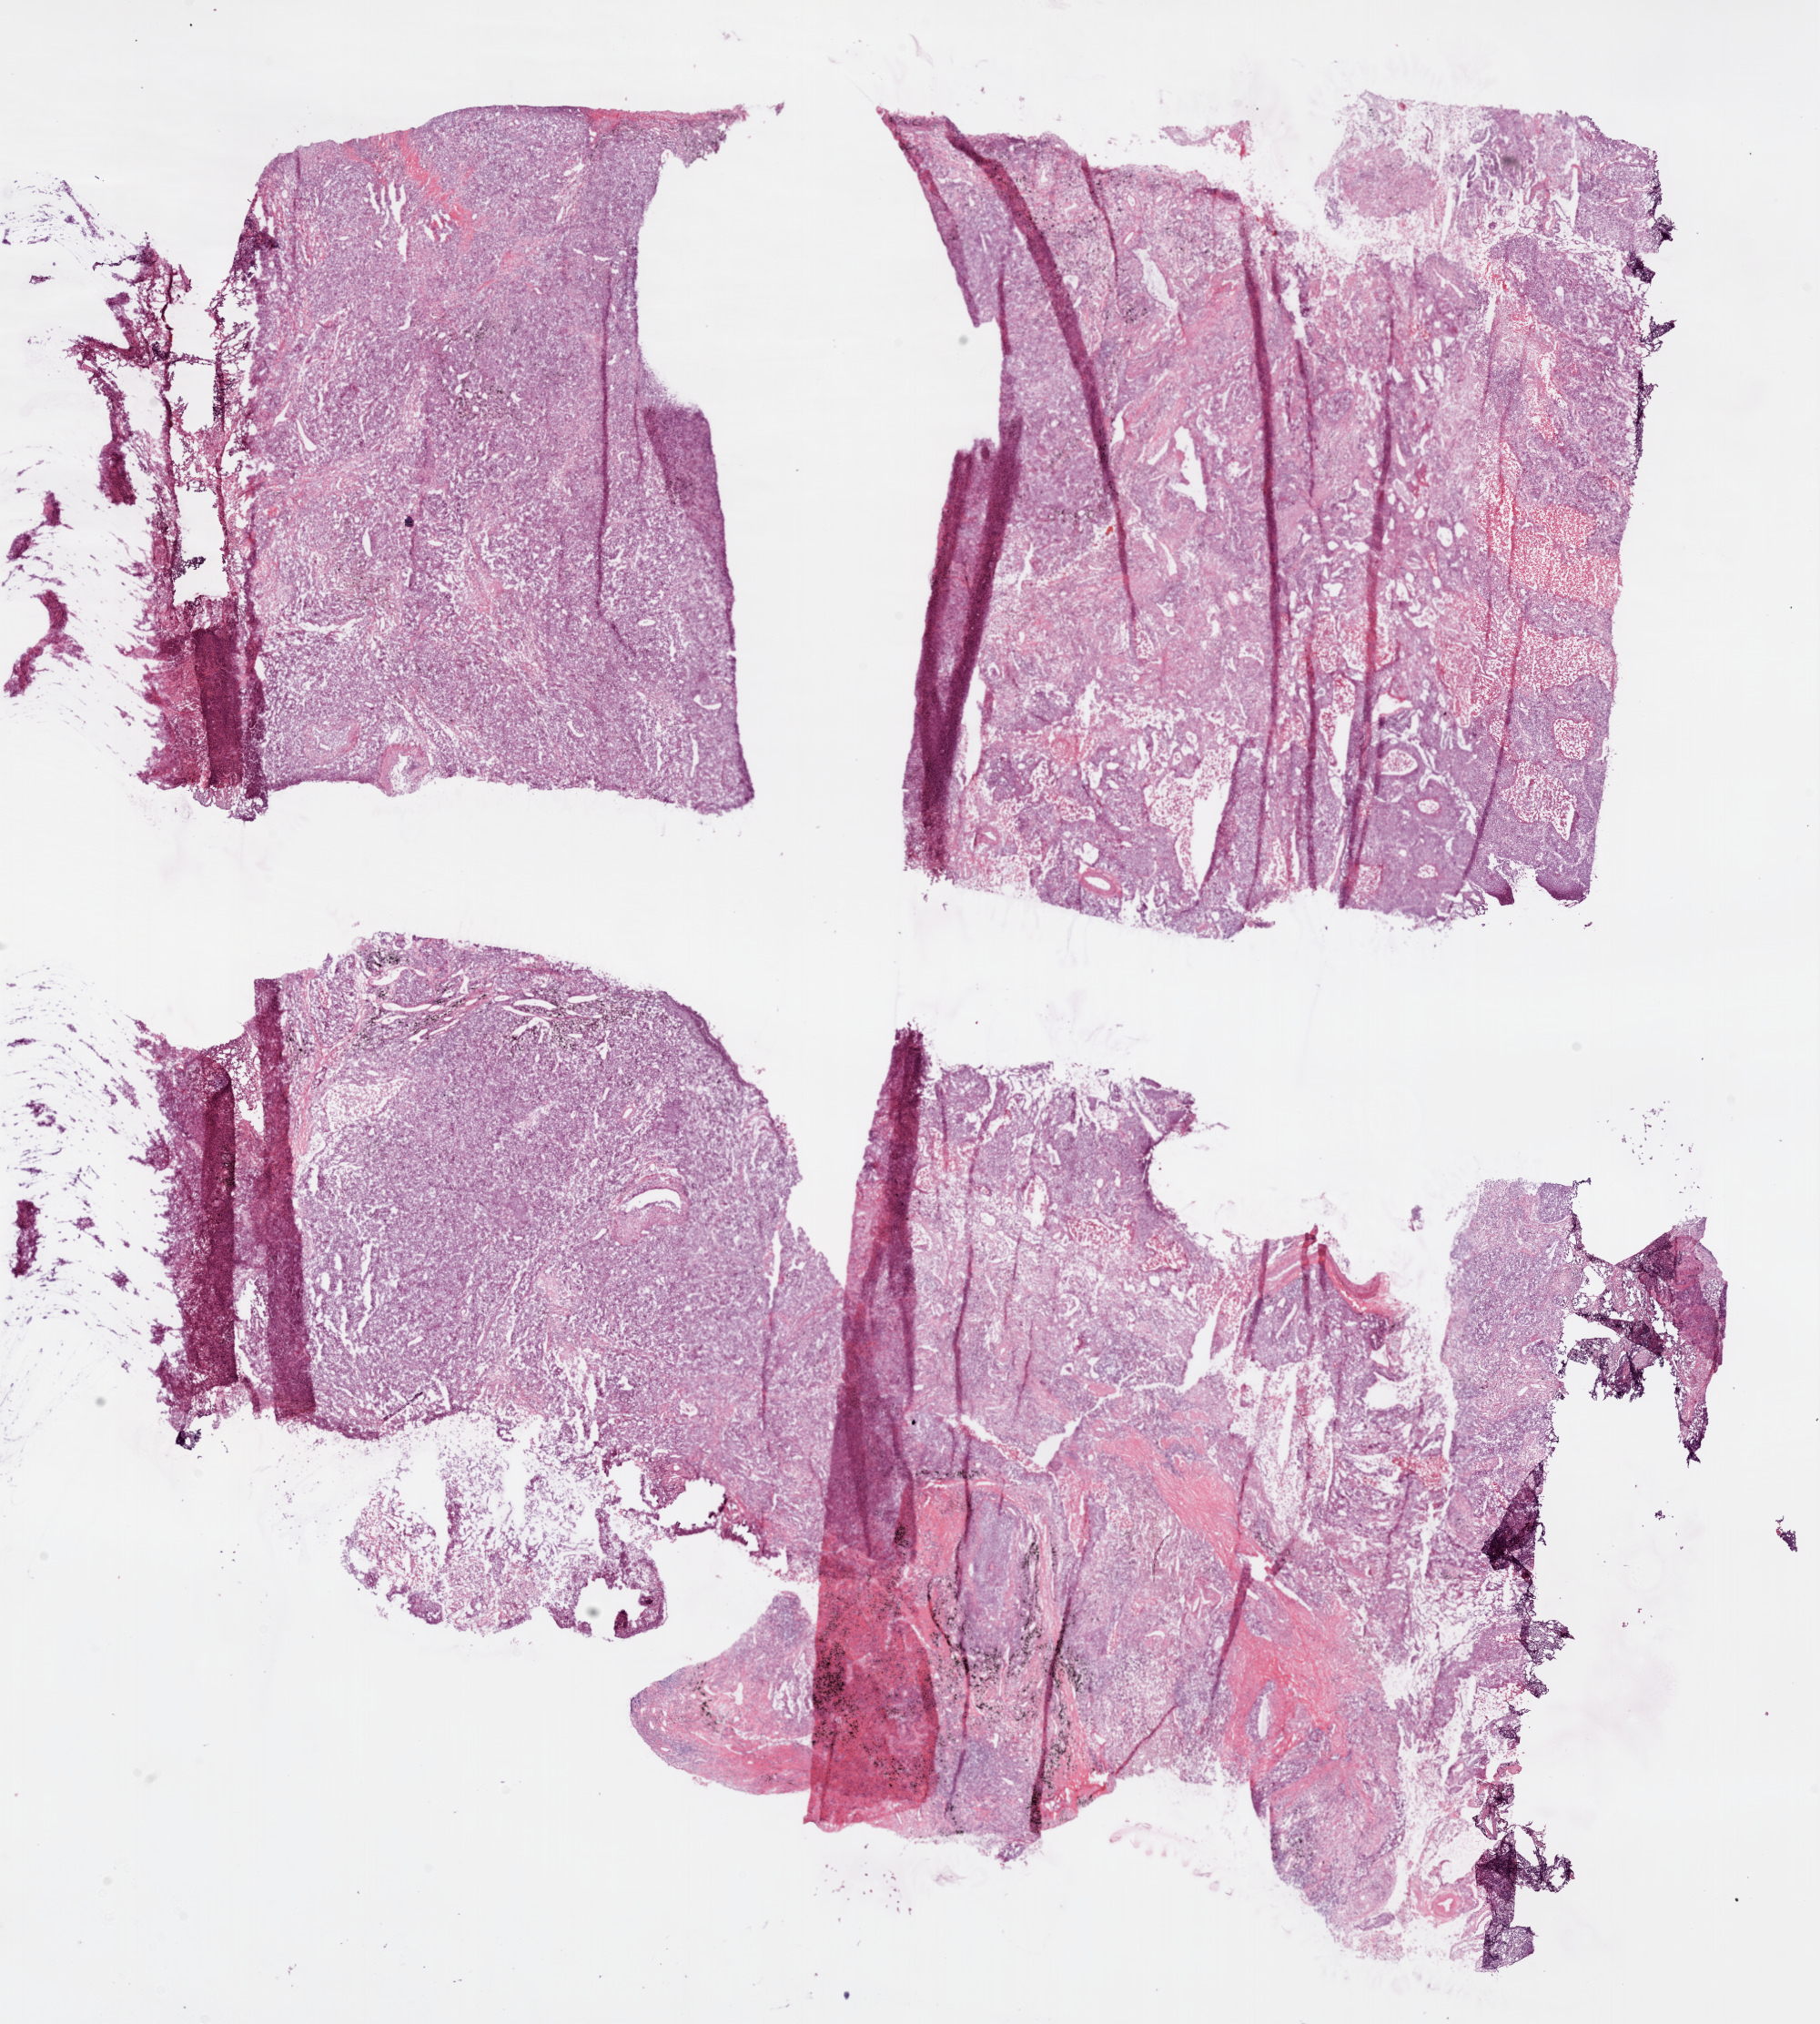
Whole-slide histology image, H&E-stained — whole scanned area (about 16.0 x 17.8 mm) shown as a low-resolution overview. Frozen section. Sample: primary tumour, lung. Male patient; age at initial diagnosis 76 years. Pathologist review of this section (percent, as recorded): tumour cells 90%, tumour nuclei 70%, normal cells 0%, stromal cells 5%, necrosis 5%. Inflammatory infiltration, as recorded: lymphocyte infiltration 10%, monocyte infiltration 2%, neutrophil infiltration 2%.
- histologic diagnosis: Squamous cell carcinoma, NOS (upper lobe, lung)
- AJCC pathologic stage: IB (7th edition)
- TNM: T2a N0 M0